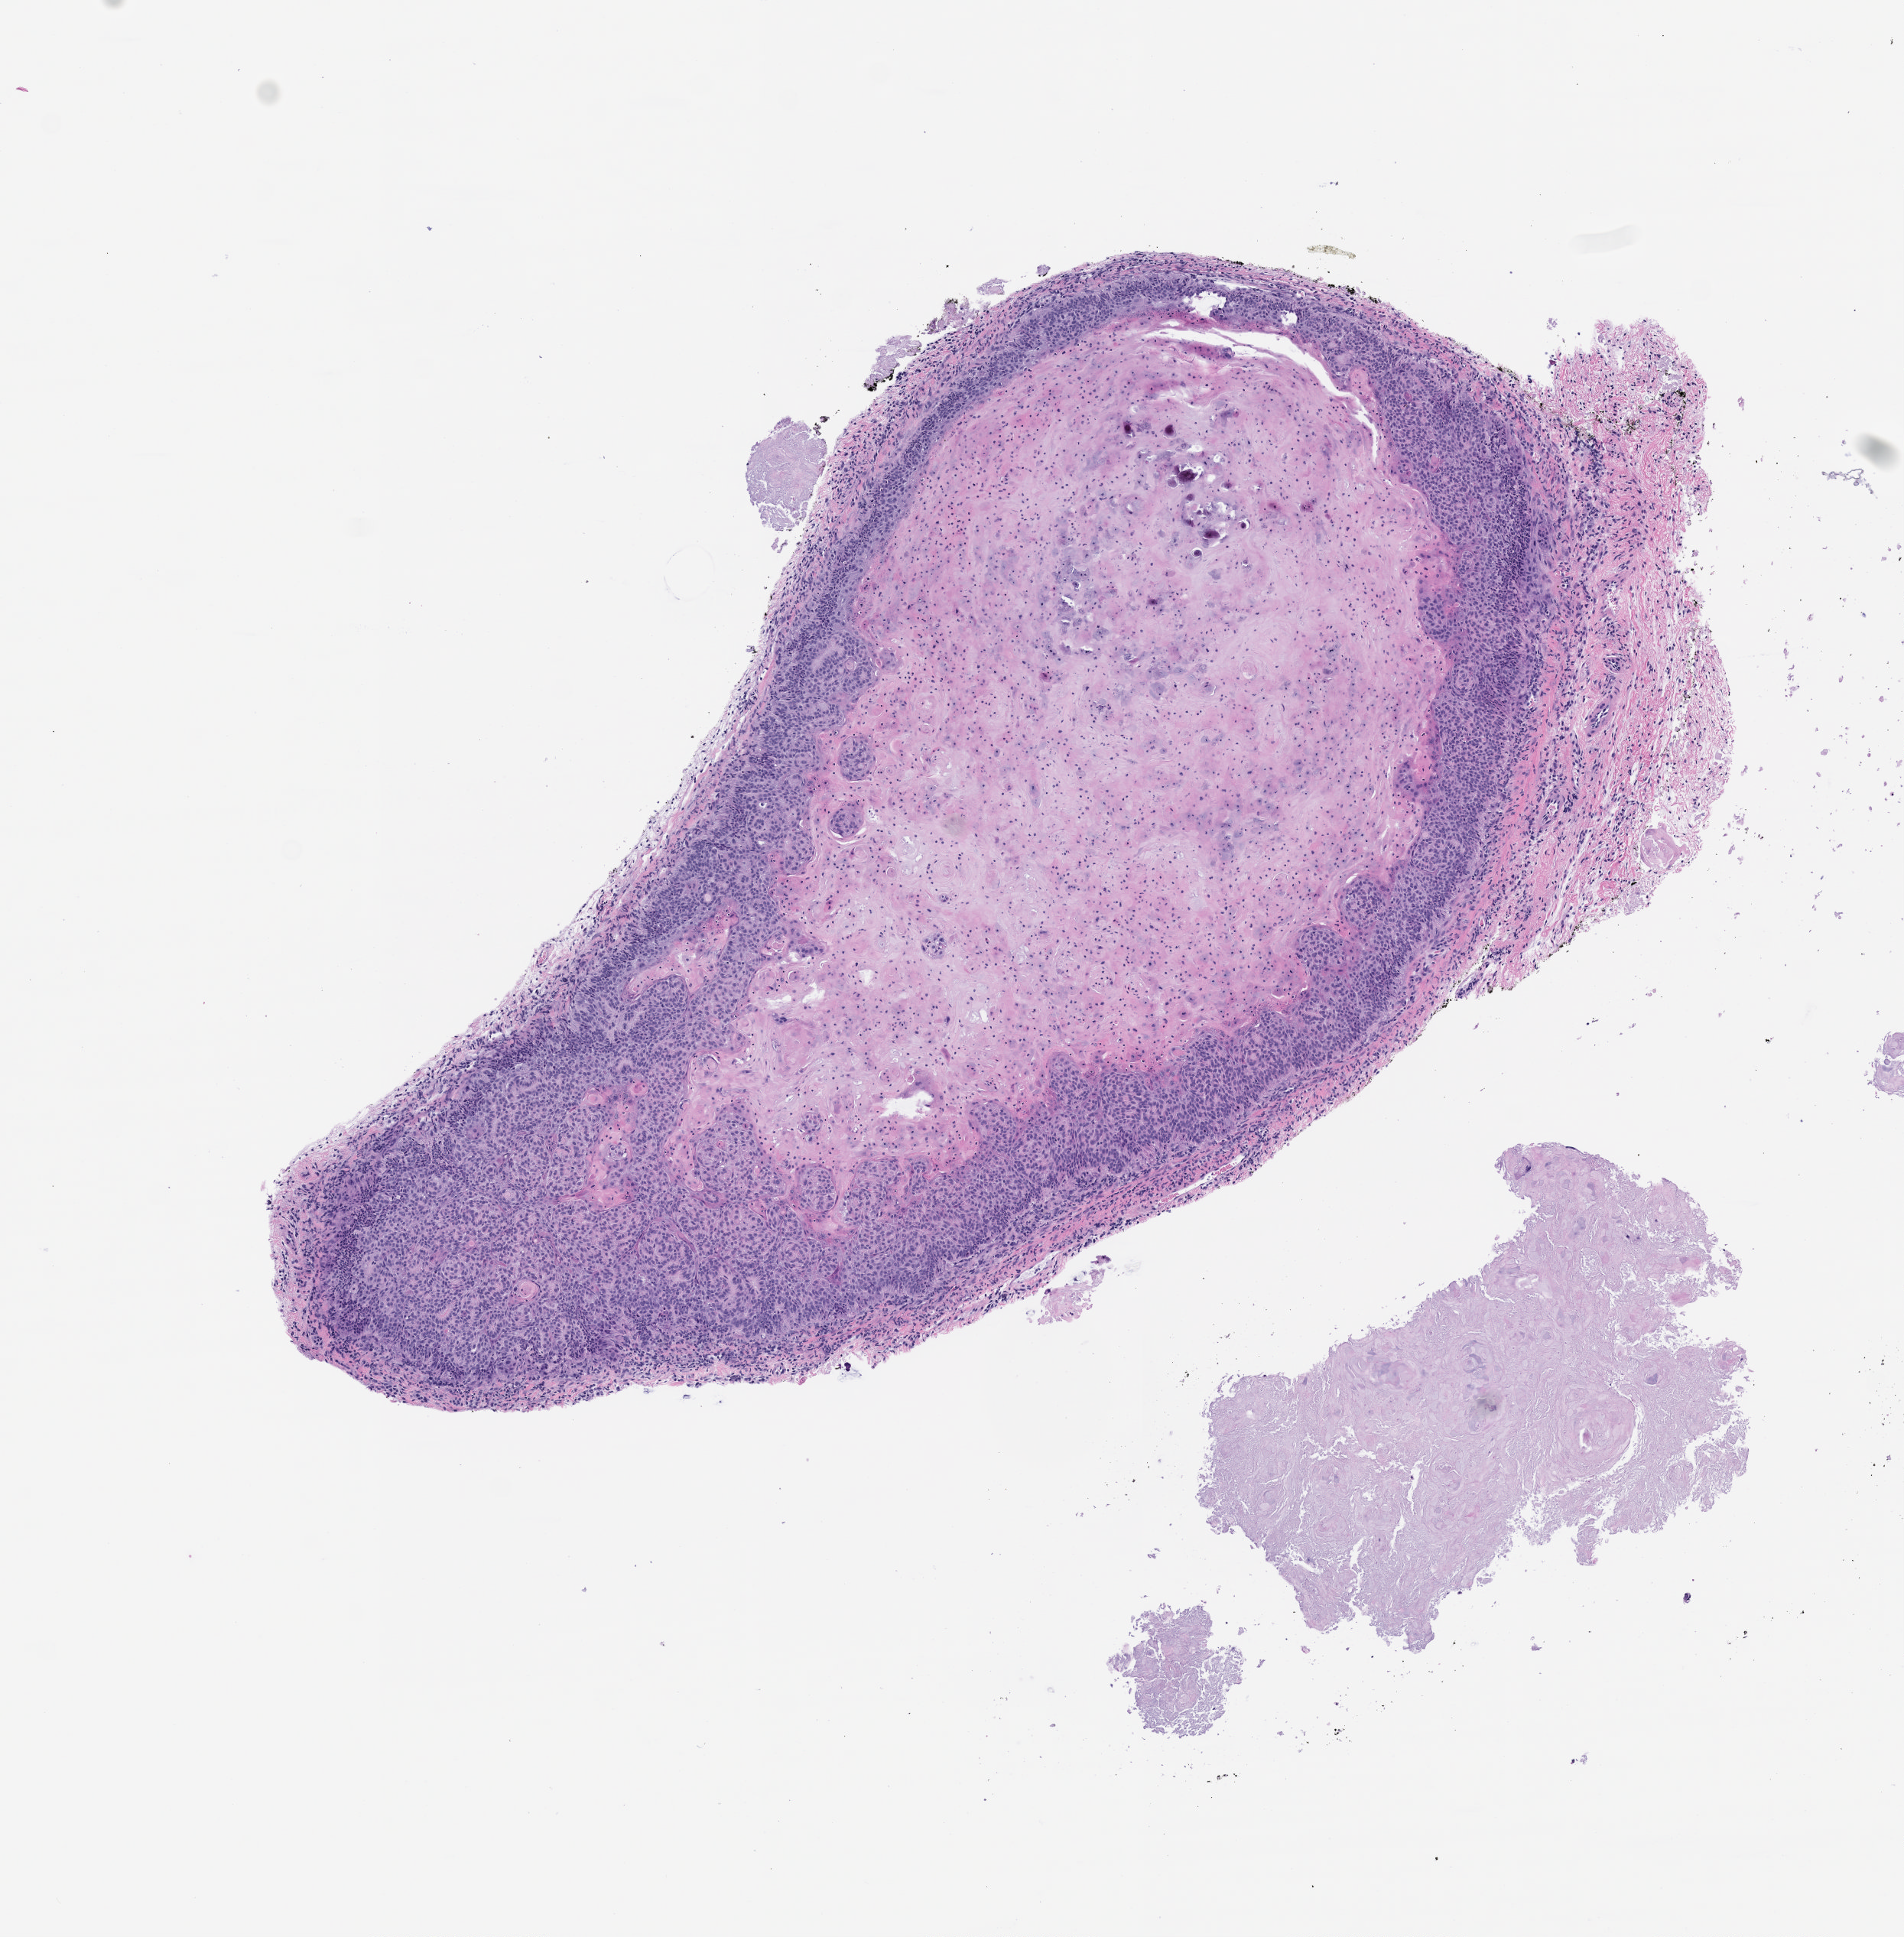
H&E whole-slide image of a patient-derived xenograft (PDX) tumor grown in a mouse, whole scanned area (about 5.0 x 5.1 mm) shown as a low-resolution overview, formalin-fixed paraffin-embedded section, tumor site category: larynx.
* originating patient diagnosis: Head and Neck Squamous Cell Carcinoma